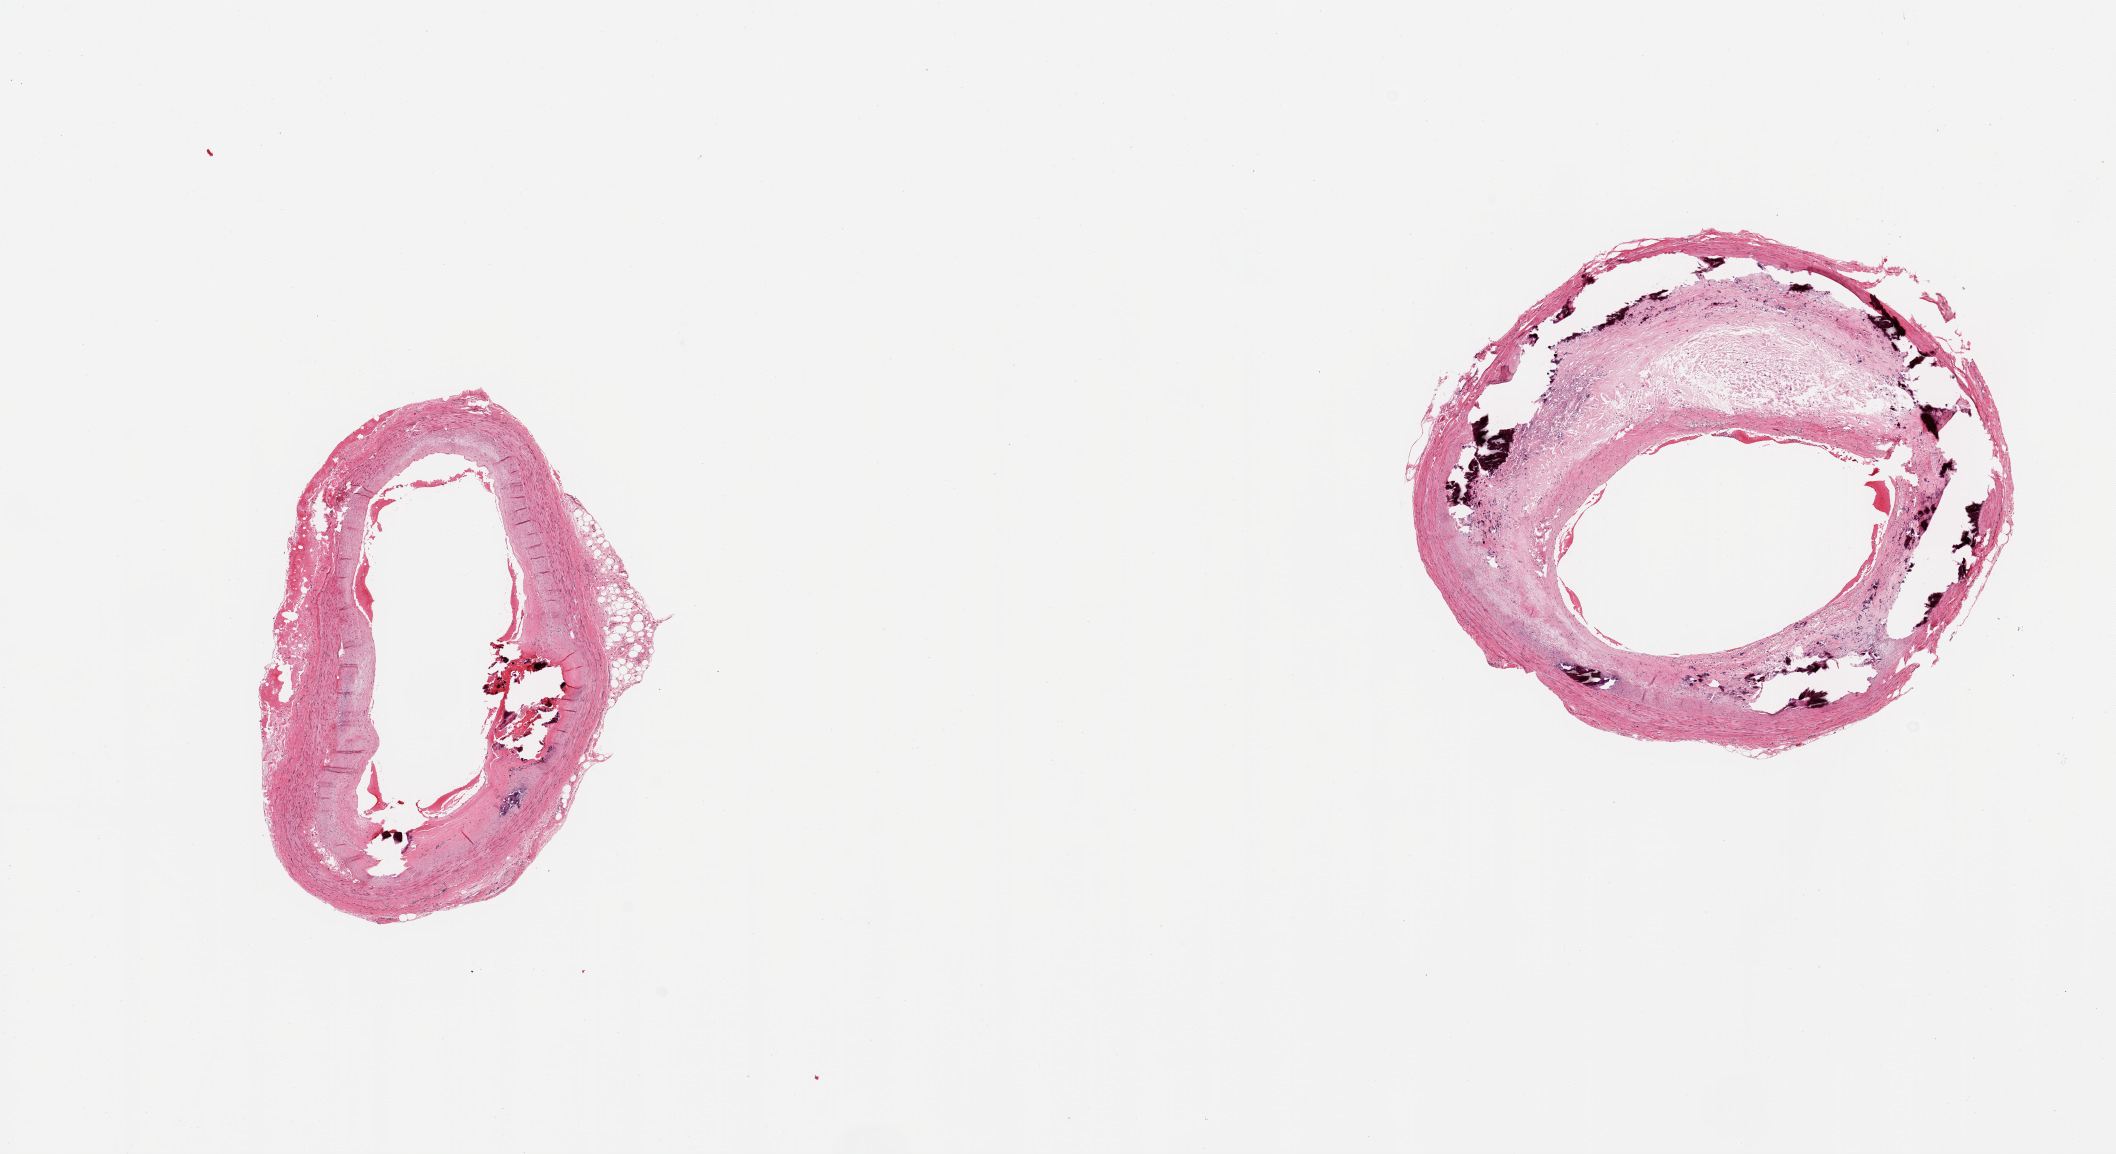
Haematoxylin and eosin whole-slide image — low-resolution overview of the scanned area, about 16.7 x 9.1 mm (slide scanned at 20x), PAXgene-fixed paraffin-embedded (PFPE) section, sampled site (target tissue): coronary artery, tissue donor sample.
* review note (as recorded): 2 pieces, ~60-70% occlusive calcified atherosis